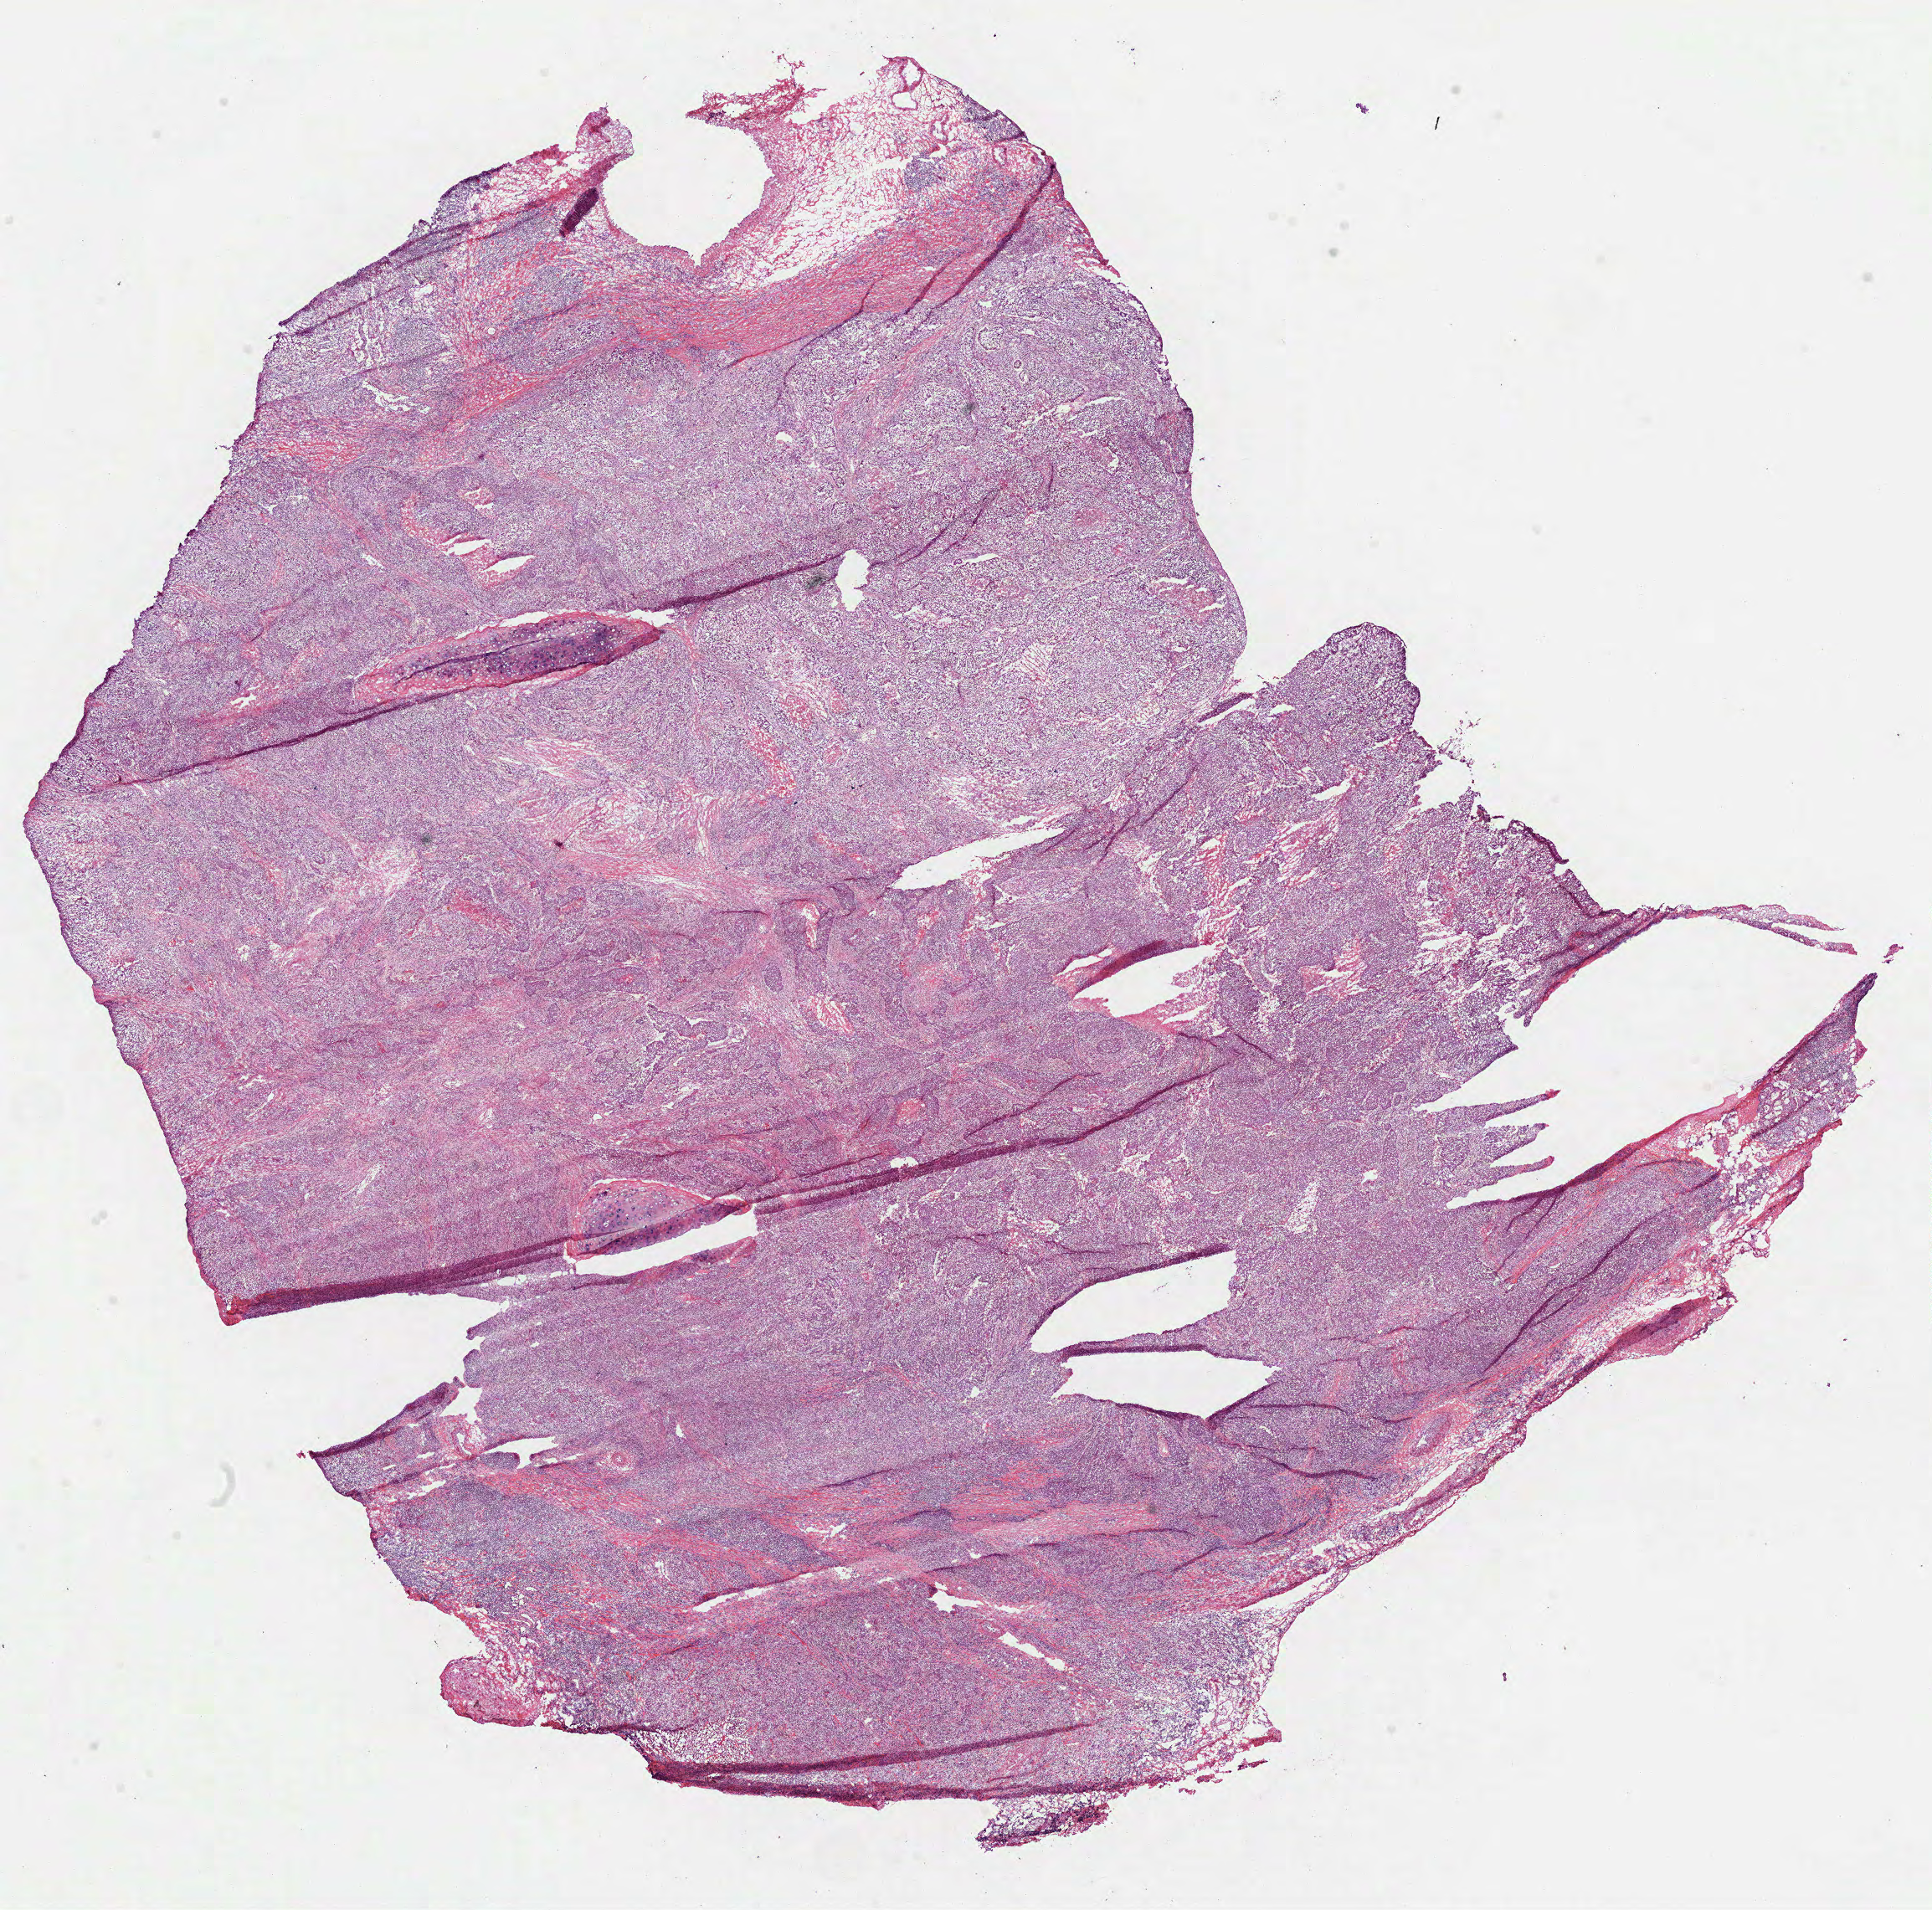
Digitized H&E-stained tissue section (whole slide), whole scanned area (about 18.6 x 18.4 mm, from a 40x scan) shown as a low-resolution overview. Frozen section from the bottom of the tissue portion. Lung, primary tumour sample. Male, age 73 years at initial diagnosis. Composition of this section per pathologist review: tumour cells 75%, tumour nuclei 68%, normal cells 2%, stromal cells 15%, necrosis 8%. Inflammatory infiltration, as recorded: lymphocyte infiltration 12%.
AJCC pathologic stage: IIIA. Laterality: left. Histologic diagnosis: Squamous cell carcinoma, NOS (upper lobe, lung).